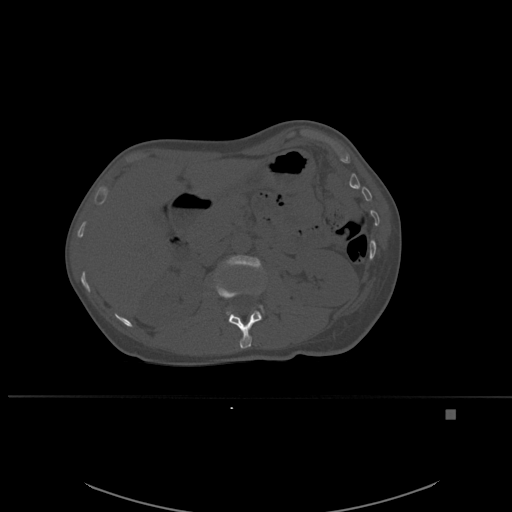
CT including the spine, one axial slice. Position 250 of 537 along the scan axis. Bone window (W 1800 / L 400 HU). 512 × 512 image matrix. Patient: female, 45 years. Case-level facts recorded for this patient, not image findings: primary cancer: lung.
Outlined on this slice (semi-automatically segmented with operator editing):
- L1 vertebra: bounding box <214,271,262,349> (left, top, right, bottom; pixels)
- L2 vertebra: <222,255,264,316>